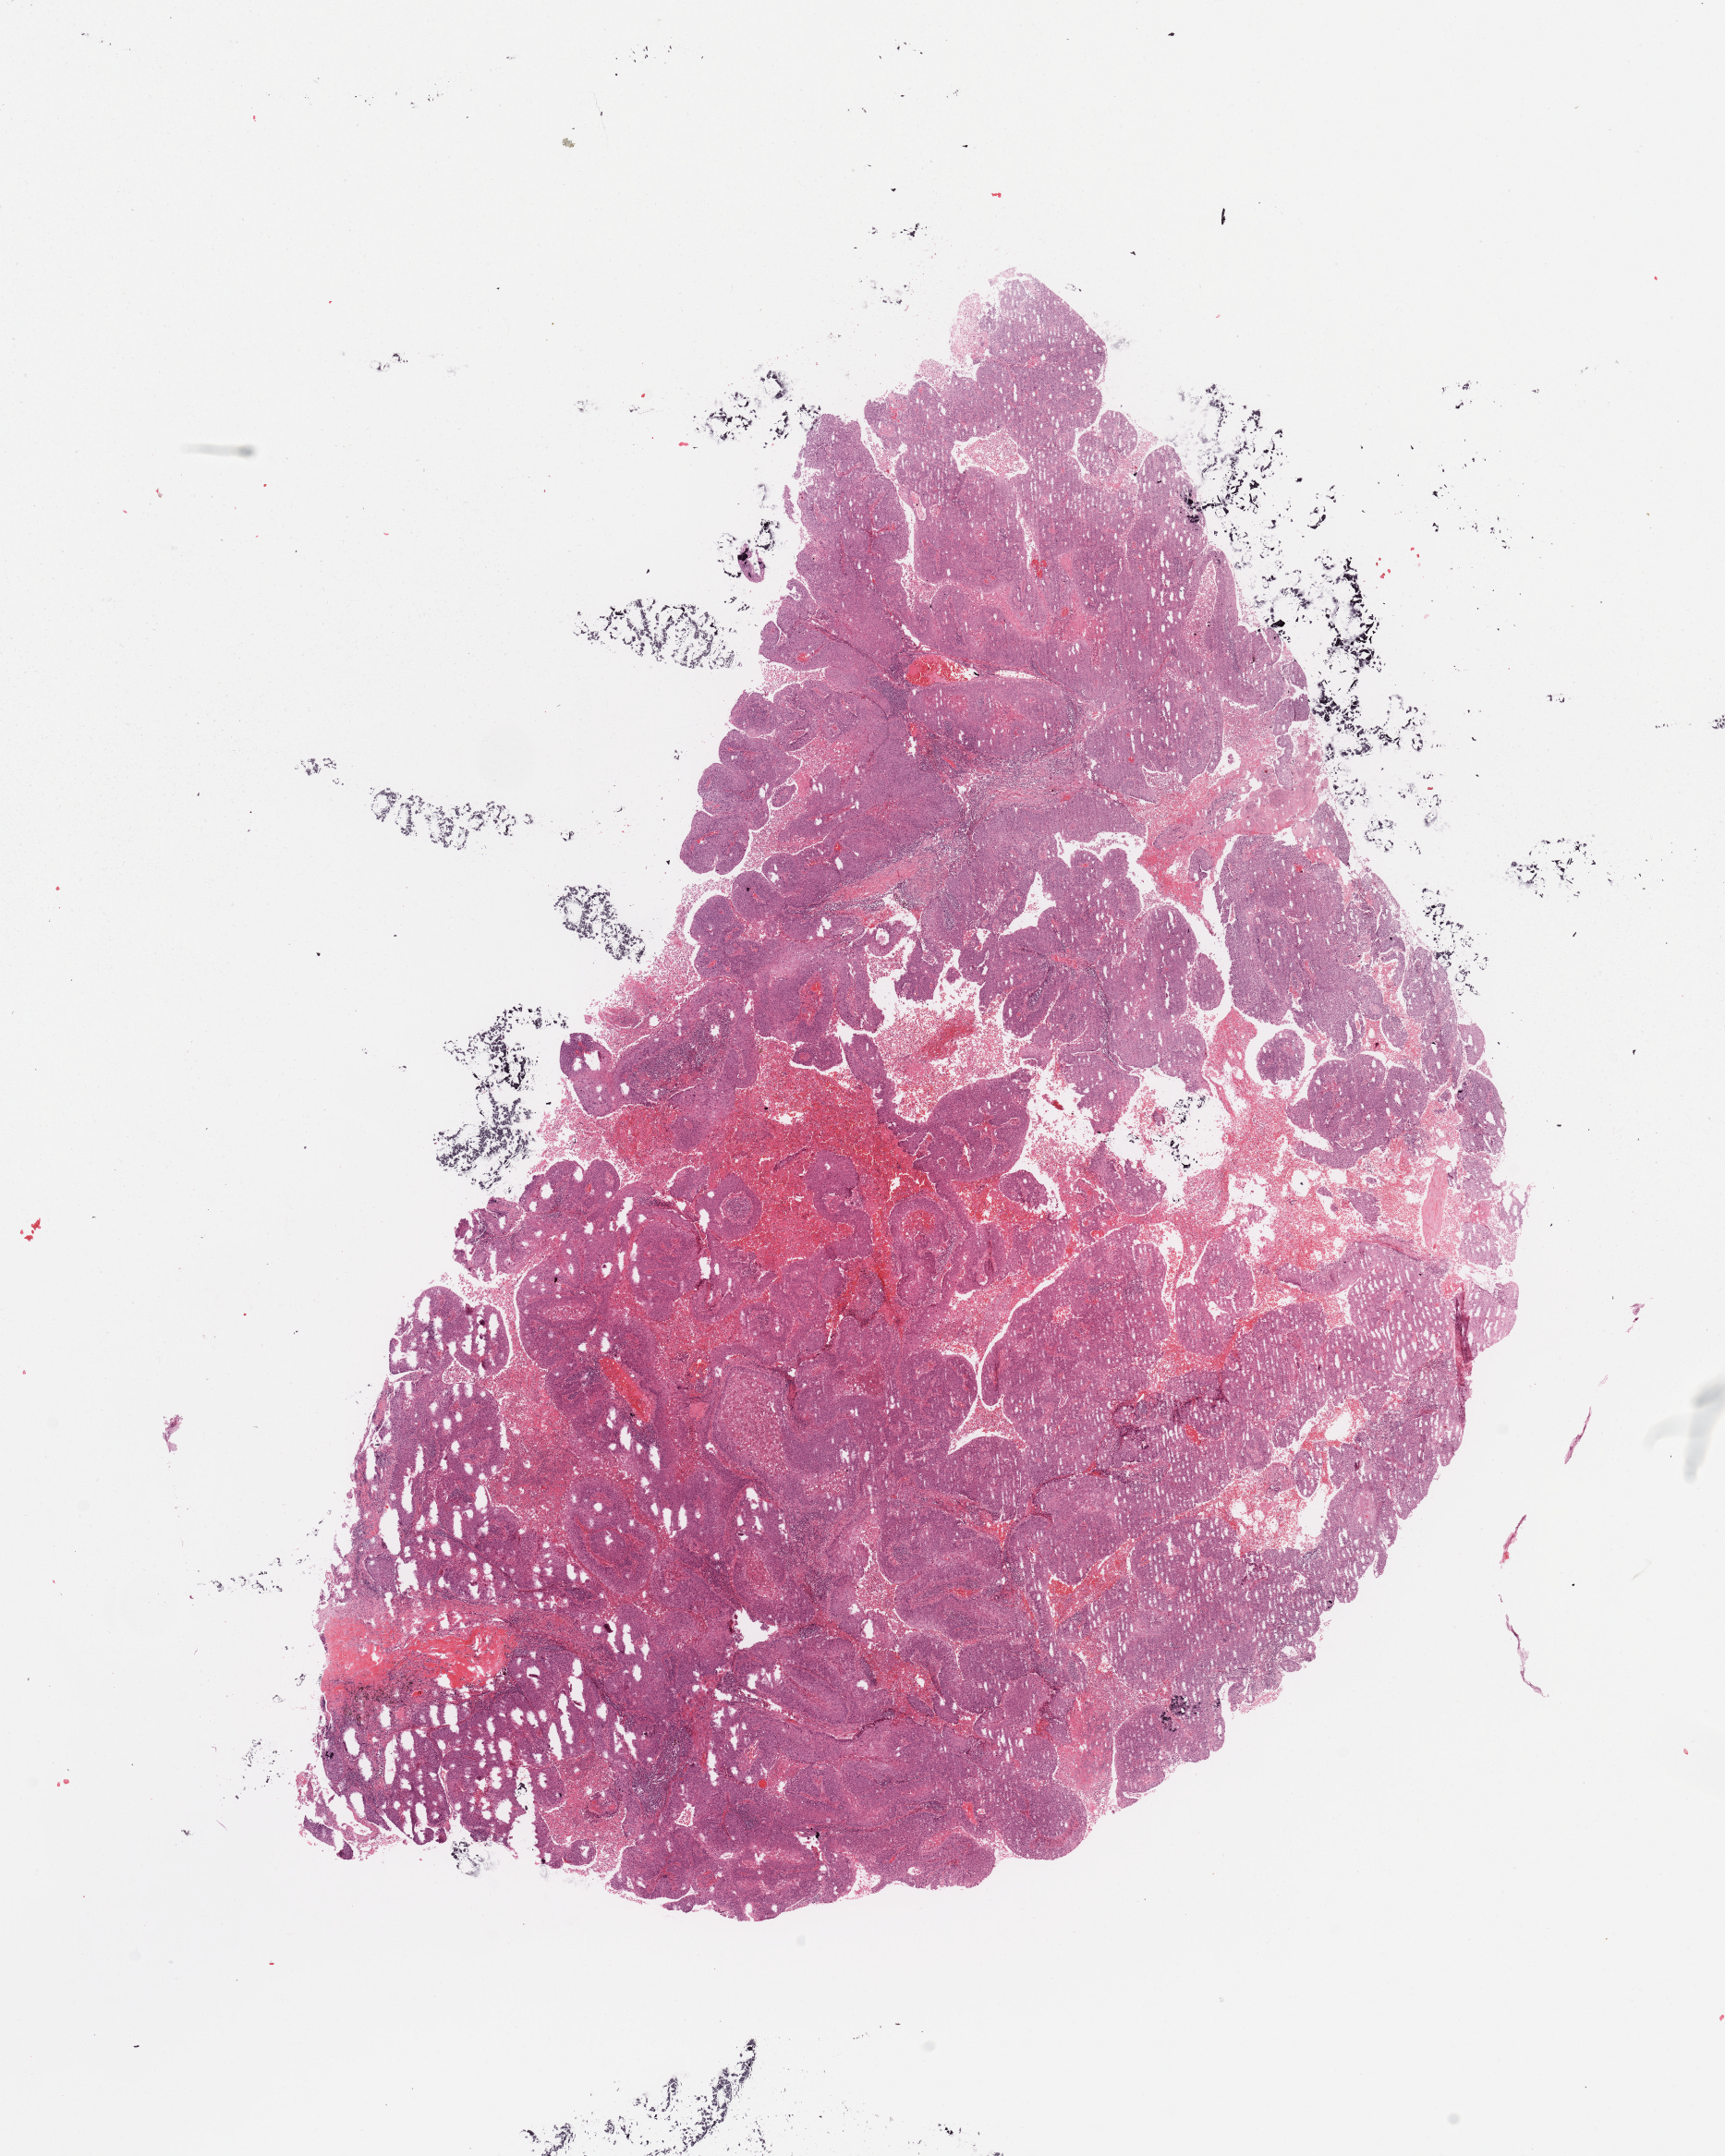
Digitized H&E-stained tissue section (whole slide) — shown as a low-resolution overview of the whole scanned area (about 14.8 x 18.5 mm, slide scanned at 20x). Tumour tissue sample, sampled site: lung. Patient: male, age 61 years. Composition of this section per pathologist review: tumour nuclei 80%, necrosis 5%.
Diagnosis: Squamous cell carcinoma, NOS.